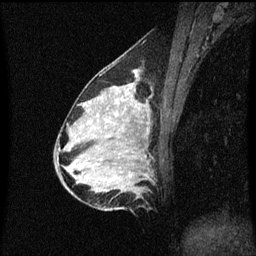
Breast MRI (dynamic contrast-enhanced), one sagittal slice; dynamic contrast-enhanced series, image 2 of 3 at this slice position (ordered by acquisition); 1.5 T; TE 4.2 ms, TR 8.4 ms; 256 × 256 image matrix, field of view 200 × 200 mm. Female patient, age 34 years. From the clinical record (not read from this slice): setting: breast cancer imaged before/during neoadjuvant chemotherapy; receptor status: HR-positive, HER2-negative.
Annotated regions visible in this slice (semi-automatic segmentation, software-assisted and operator-edited):
- analysis volume of interest (the breast-tissue region the enhancement analysis was run in; not a lesion): bounding box (x1, y1, x2, y2) in pixels: (69, 70, 153, 209)
- tumour enhancement mask (voxels above the 70 % enhancement threshold inside the analysis volume of interest): (108, 72, 140, 181)